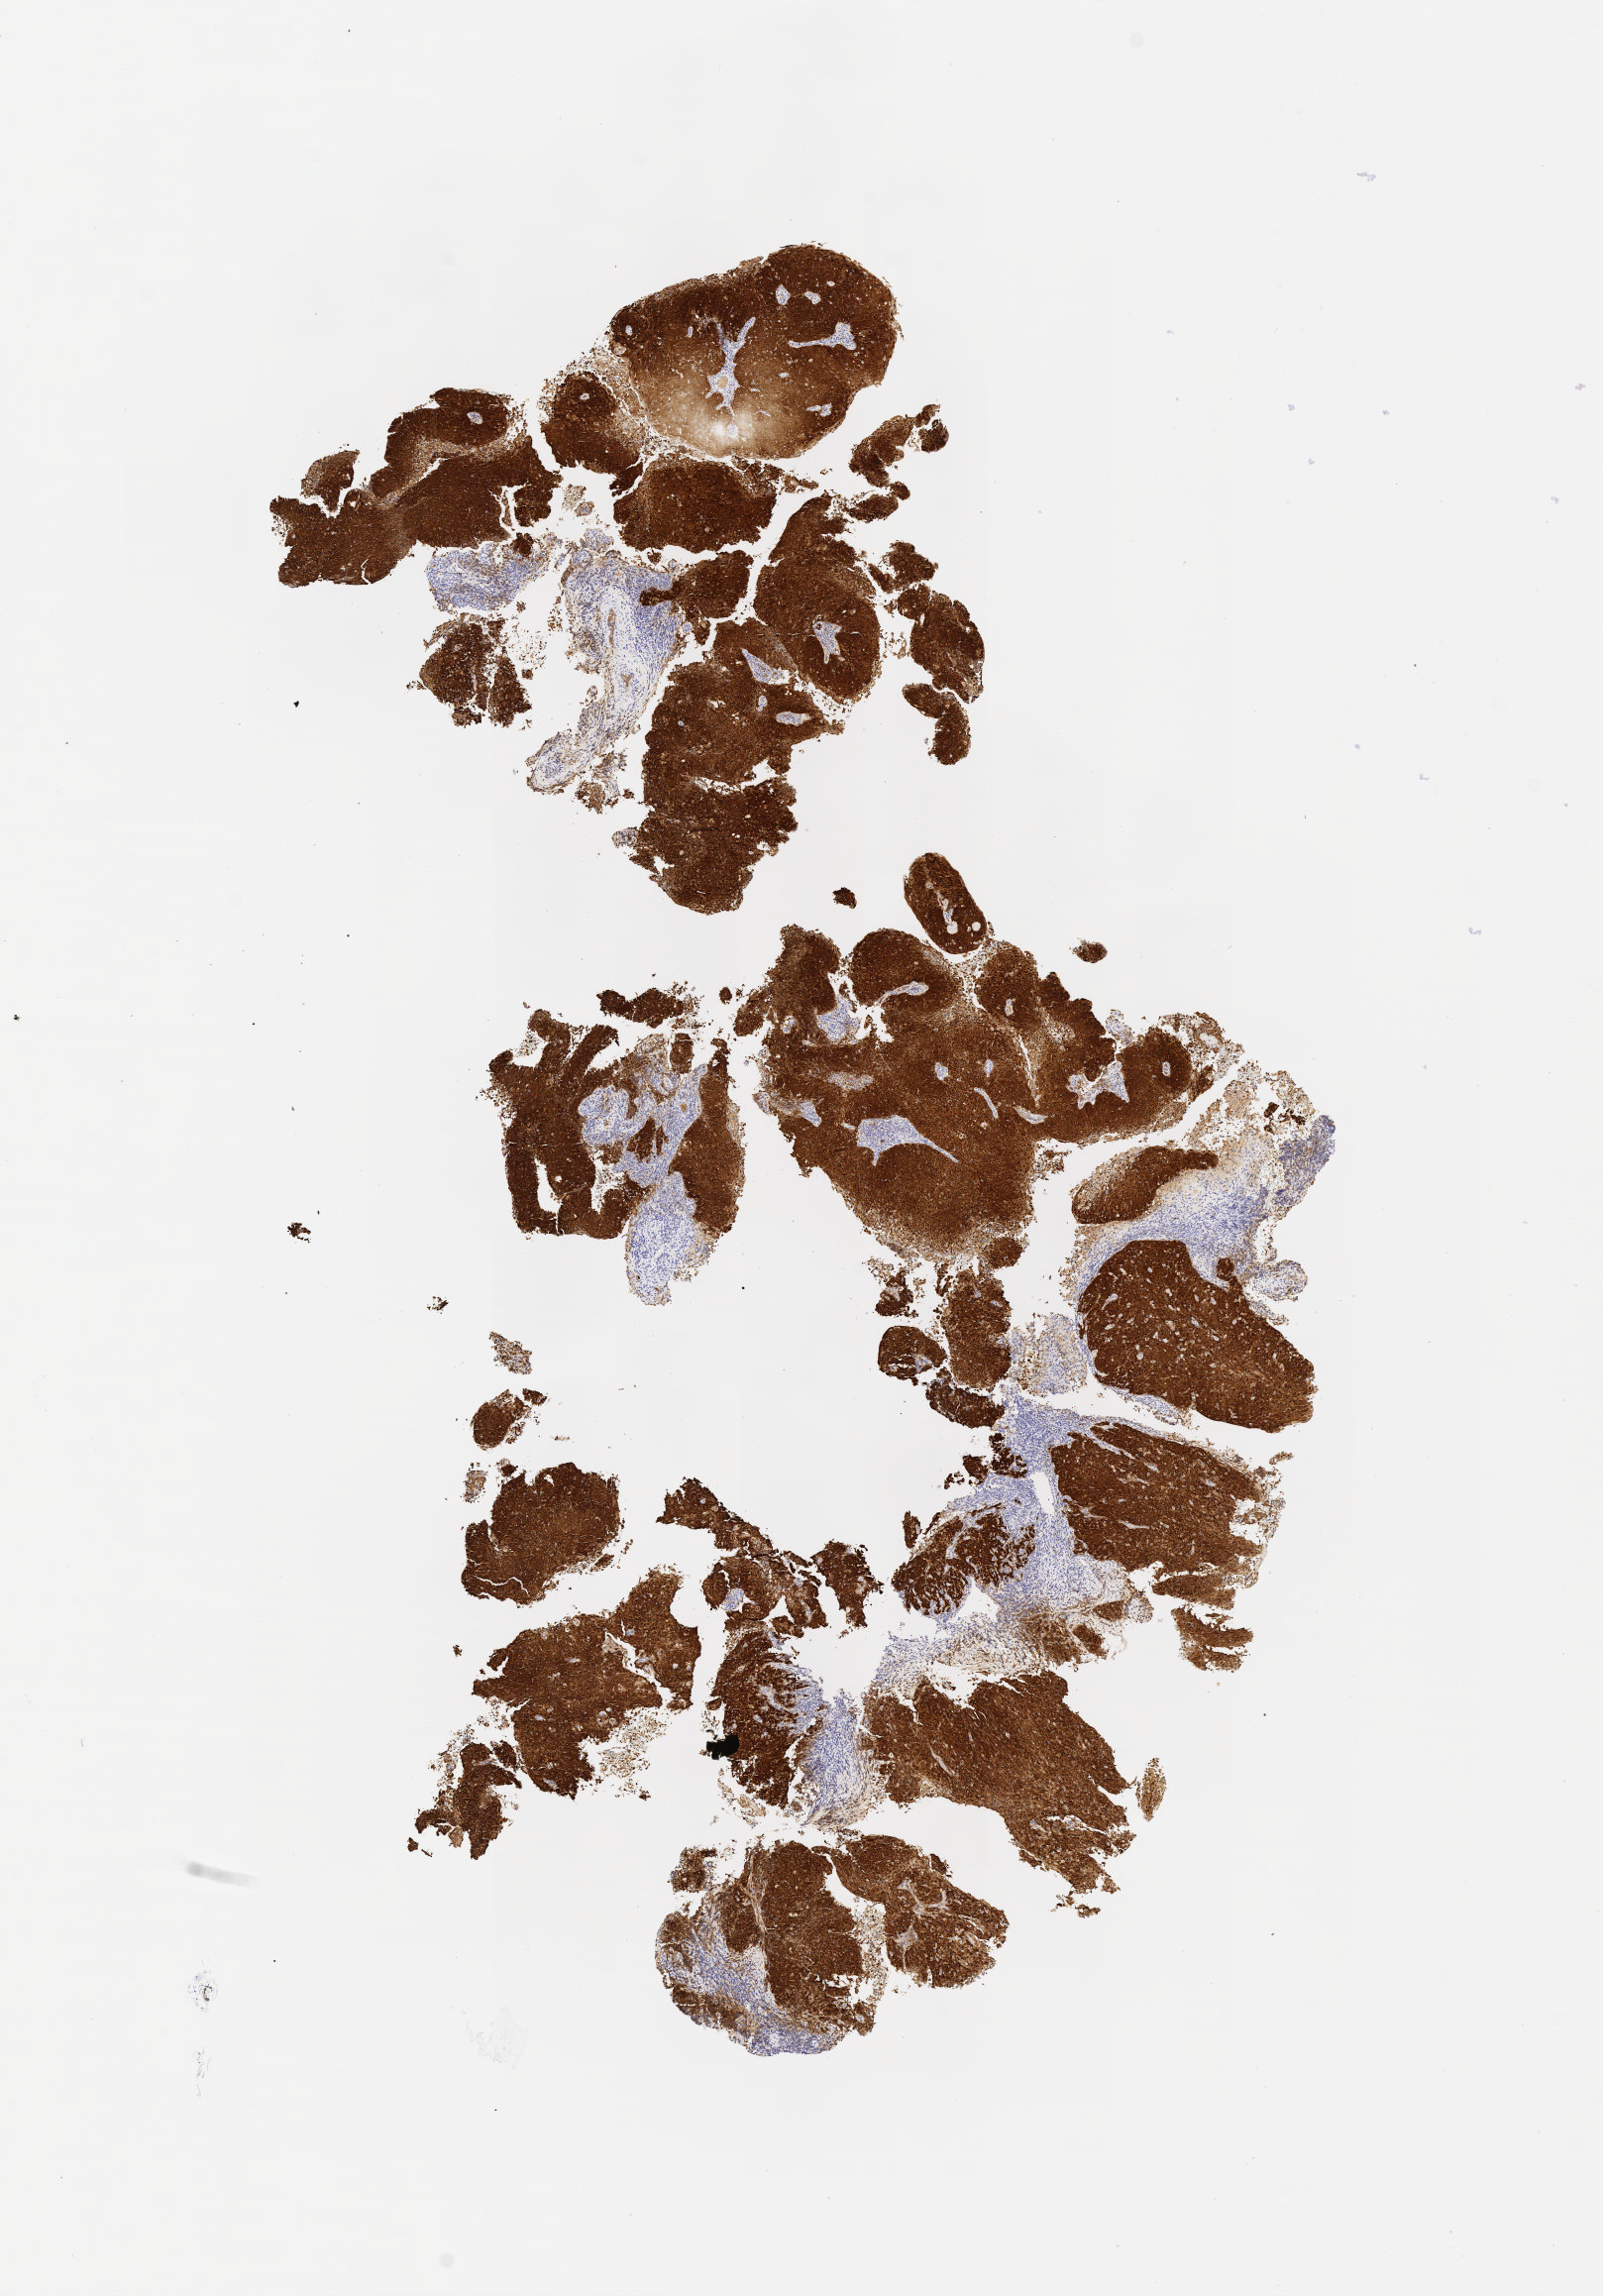
Whole-slide image, immunohistochemical stain for p16 (p16INK4a) — shown as a low-resolution overview of the whole scanned area (about 6.5 x 9.4 mm), tumor tissue, anatomic site: cervix. Female patient, age 56 years.
Histologic diagnosis: Squamous cell carcinoma, large cell, nonkeratinizing, NOS.